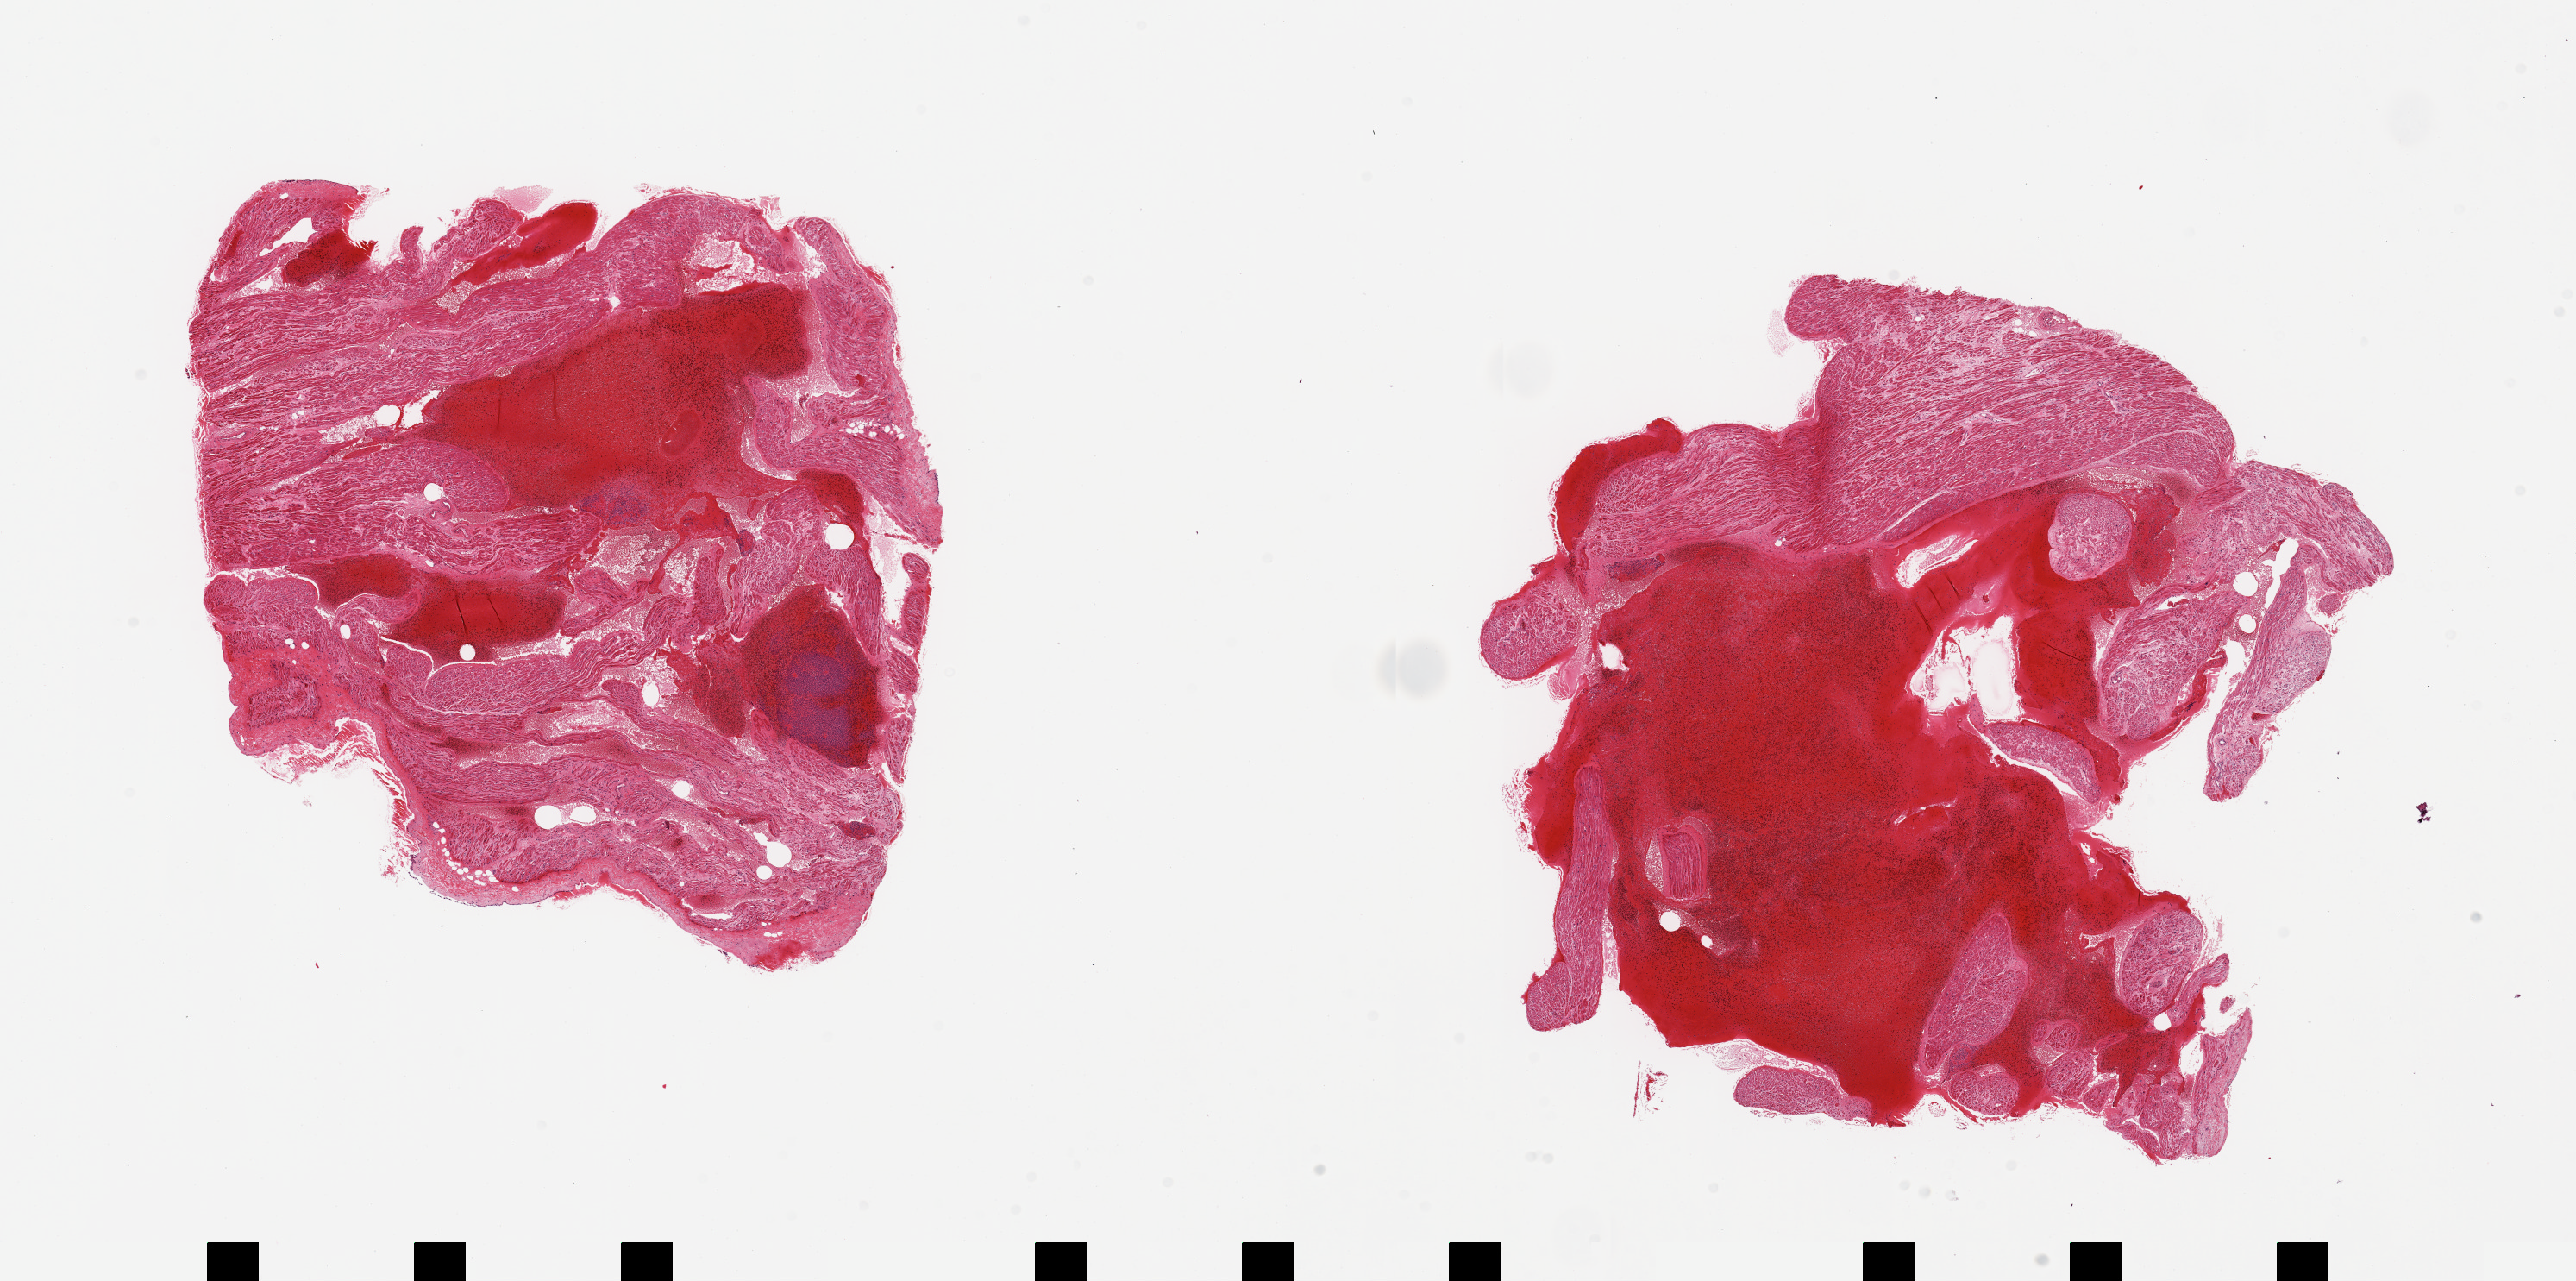
Whole-slide image, H&E stain — a low-resolution overview of the entire scanned area, about 23.6 x 11.7 mm. PAXgene-fixed, paraffin-embedded tissue. Target tissue: auricular appendage. Donor tissue sample. Donor: male.
Pathologist's review note for this sample: 2 pieces; large portion of both is blood/clot.